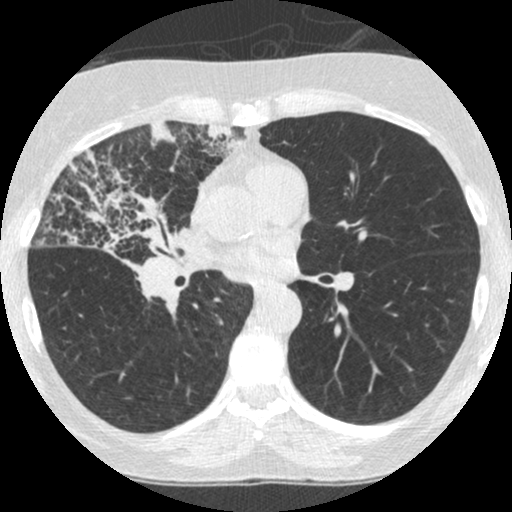
Low-dose screening chest CT, one axial slice. Position 138 of 253 along the scan axis. 120 kVp. Lung window (W 1500 / L -600 HU). 1.25 mm slice thickness. 512 × 512 image matrix.
Structures marked on this image (manually delineated by an expert):
- lesion 2 (tumor, hilum of right lung): bounding box [x1, y1, x2, y2] px = [42, 155, 189, 272]
- lesion 3 (tumor, upper lobe of right lung): [149, 121, 178, 149]
- lesion 4 (tumor, upper lobe of right lung): [204, 123, 244, 158]